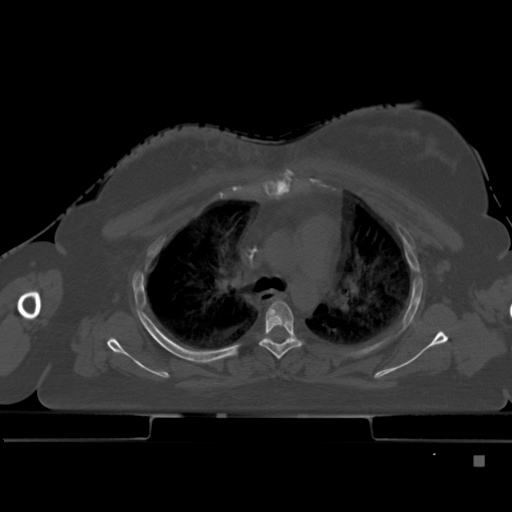
CT including the spine, one axial slice; slice 332 of 495 in the series (ordered by position); bone window (W 1800 / L 400 HU); 1.5 mm slice thickness; 512 × 512 image matrix, field of view 404 × 404 mm. Female patient, age 33 years. Case-level facts recorded for this patient, not image findings: primary cancer: breast; vertebrae with lytic lesions (as recorded): T1.
Structures marked on this image (semi-automatic segmentation, software-assisted and operator-edited):
- T4 vertebra: box from (x=260, y=301) to (x=301, y=360) px